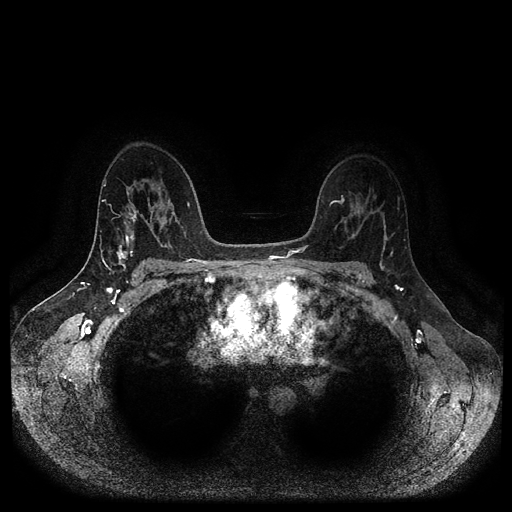
Breast MRI (dynamic contrast-enhanced, multi-phase), one axial slice; slice 67 of 116 in the series (ordered by position); dynamic contrast-enhanced series, time point 2 of 5 at this slice position (early post-contrast); 1.5 T; TE 2.6 ms, TR 5.3 ms; 2 mm slice thickness; 512 × 512 image matrix, field of view 360 × 360 mm. Female patient, age 45 years.
Annotated regions visible in this slice (semi-automatically segmented with operator editing):
- breast lesion (labelled 'tumour' in the annotation; benign lesions carry a separate 'benign' label): bounding box [x1, y1, x2, y2] px = [116, 245, 128, 268]